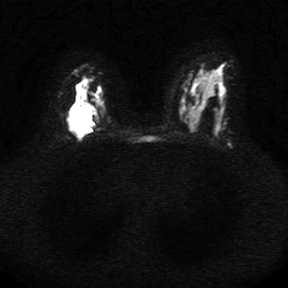
Breast MRI, one axial slice. Slice 19 of 34 in the series (ordered by position). Diffusion-weighted series; image 2 of 4 stored at this slice position (different b-values; order by instance number). 1.5 T. 5 mm slice thickness. 288 × 288 image matrix, field of view 340 × 340 mm. Female patient.
Outlined on this slice (expert manual segmentation):
- tumour on diffusion-weighted imaging: bounding box (x1, y1, x2, y2) in pixels: (64, 104, 93, 134)